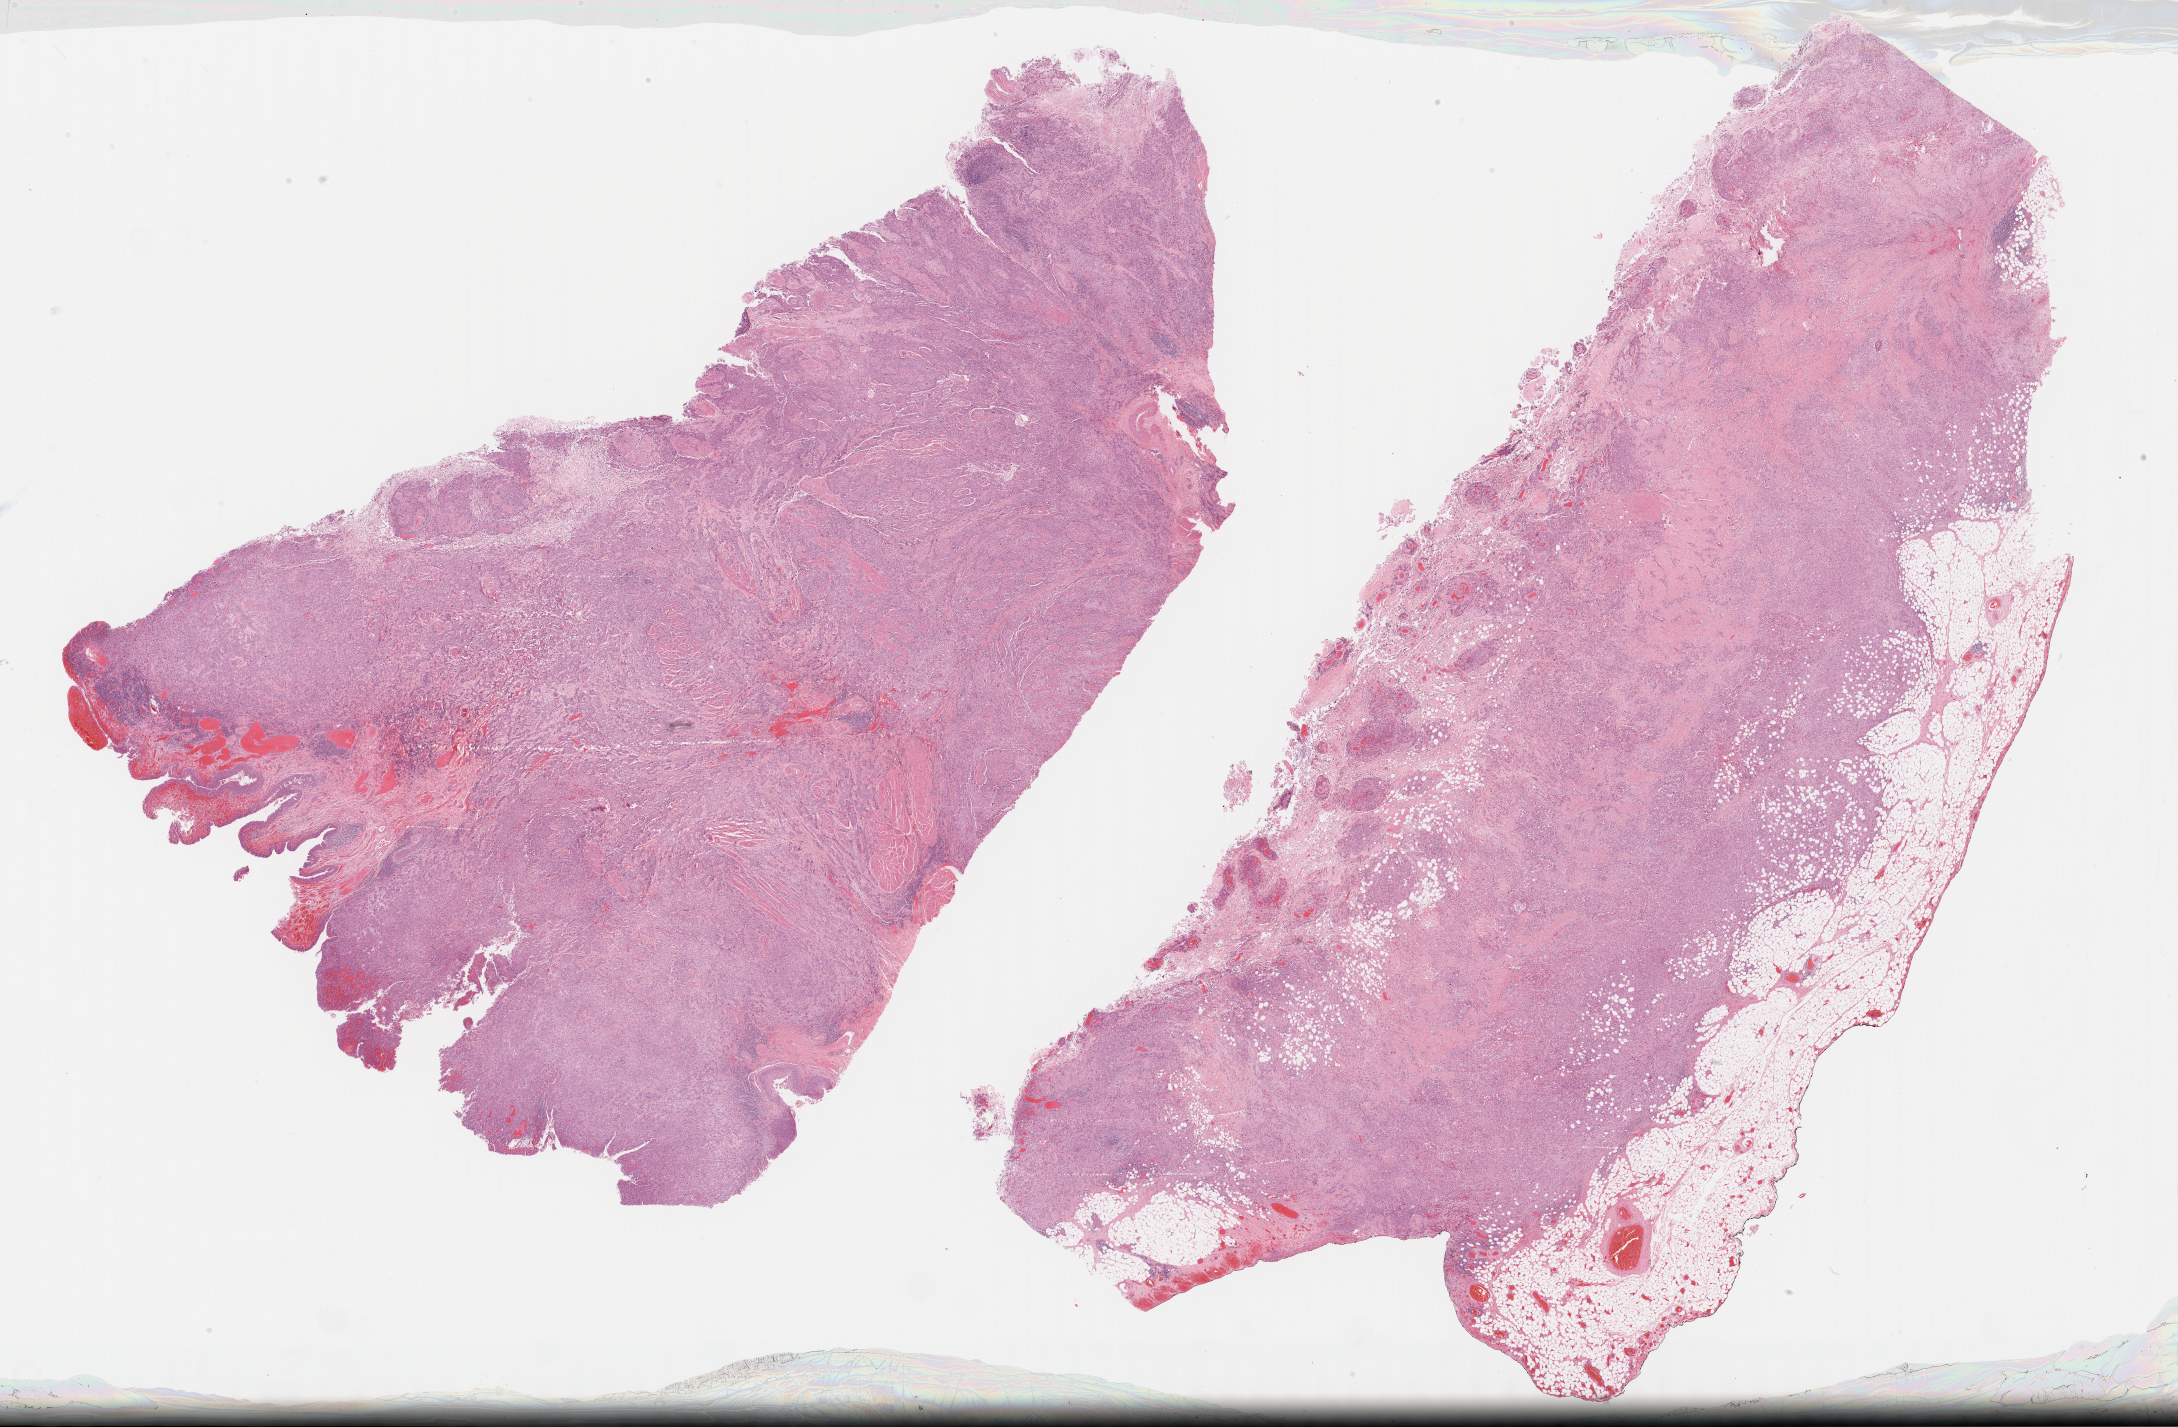
Whole-slide histology image, H&E — a low-resolution overview of the entire scanned area, about 35.2 x 23.1 mm; FFPE section; sample: primary tumour, bladder. Patient: male, age at initial diagnosis 63 years. Histologic grade: high grade.
Histologic diagnosis: Transitional cell carcinoma. TNM: T3a N1 MX. AJCC pathologic stage: IV.